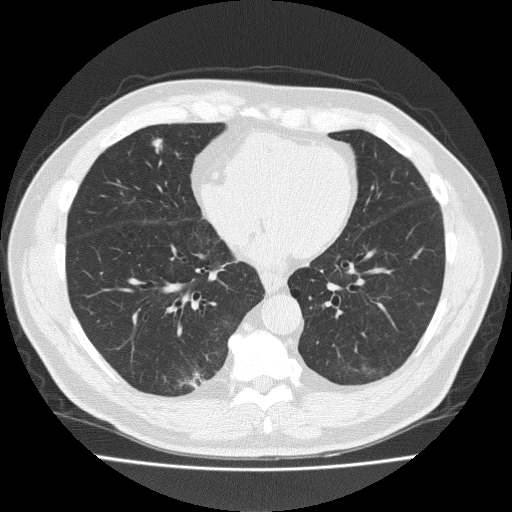
Low-dose screening chest CT, axial slice, second annual screen, lung window (W 1500 / L -600 HU). Male, age 57 years at enrolment. Current smoker at enrolment.
Lesion marked by an expert reader, bounding box (x1, y1, x2, y2) in pixels: (134, 131, 176, 169). The exam's reader record, not a measurement of the box and not confirmed to be the same lesion: non-calcified nodule or mass ≥4 mm, right middle lobe, 8 × 7 mm, spiculated (stellate) margins, soft tissue attenuation, pre-existing on the prior screen: yes; interval growth: yes. Later outcome: lung cancer diagnosed 67 days after this screen — adenocarcinoma, NOS, right middle lobe, moderately differentiated (G2), stage IA (AJCC 6th edition), 12 mm at pathology.